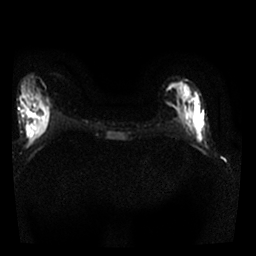
Breast MRI, one axial slice; position 9 of 25 along the scan axis; diffusion-weighted series; image 2 of 4 stored at this slice position (different b-values; order by instance number); 1.5 T; 4 mm slice thickness; 256 × 256 image matrix. Female patient.
Structures marked on this image (expert manual segmentation):
- tumour on diffusion-weighted imaging: bounding box (x1, y1, x2, y2) in pixels: (186, 91, 206, 145)